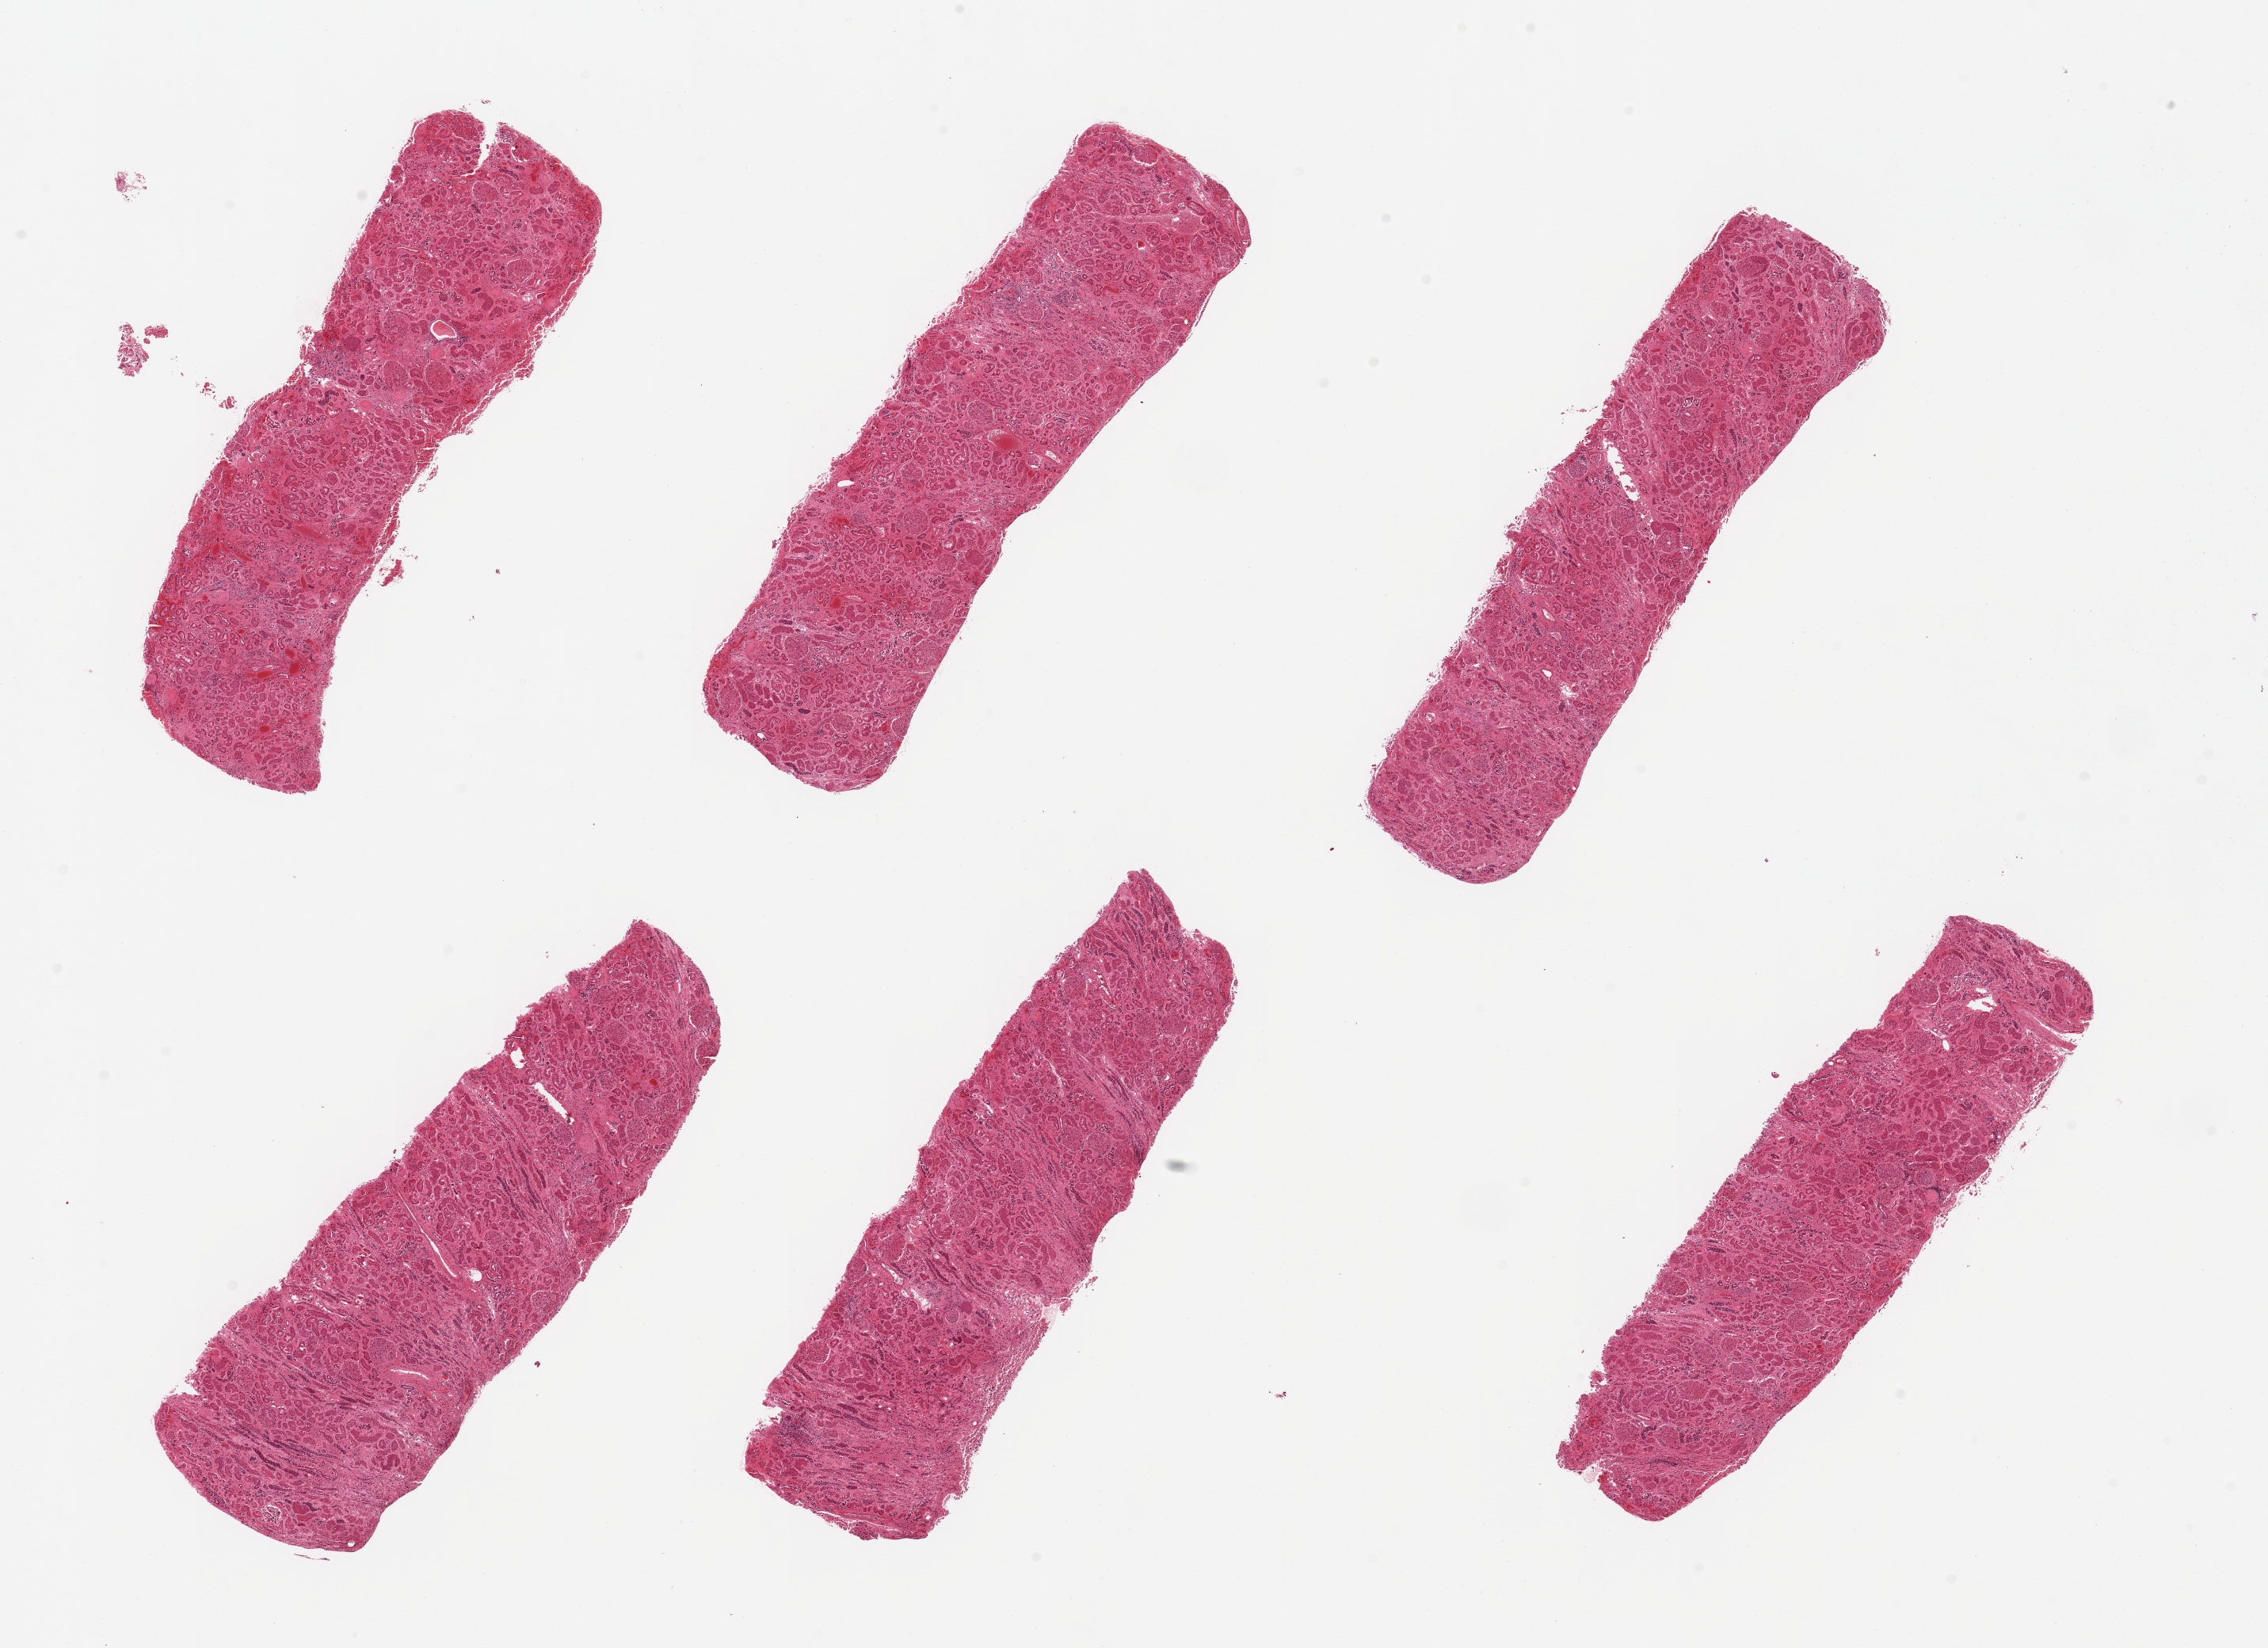
Digitized hematoxylin and eosin (H&E)-stained section, brightfield — shown as a low-resolution overview of the whole scanned area (about 22.6 x 16.4 mm, slide scanned at 20x). PAXgene-fixed paraffin-embedded (PFPE) section. Sampled site (target tissue): renal cortex. Donor tissue sample. Male donor.
• review note (as recorded): 6 pieces; moderate interstitial fibrosis; tubules largely autolyzed